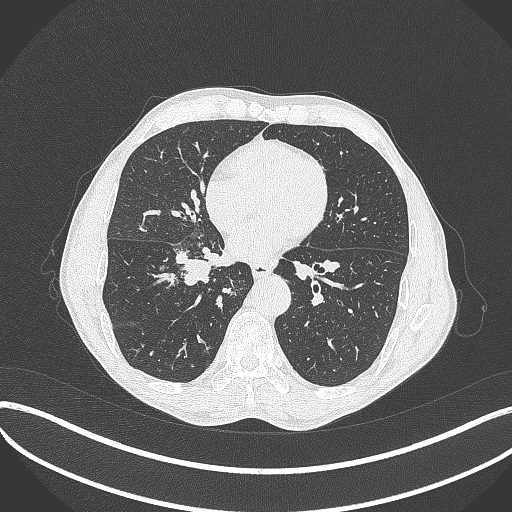
Chest CT, one axial slice; slice 185 of 481 in the series (ordered by position); lung window (W 1500 / L -600 HU); 1 mm slice thickness; 512 × 512 image matrix. Male patient, age 65 years. Case-level facts recorded for this patient, not image findings: clinical TNM (as recorded): T2a N0 M0.
Structures marked on this image (bounding box drawn by a radiologist):
- lung tumour (recorded histology: squamous cell carcinoma): bounding box <173,246,220,285> (left, top, right, bottom; pixels)